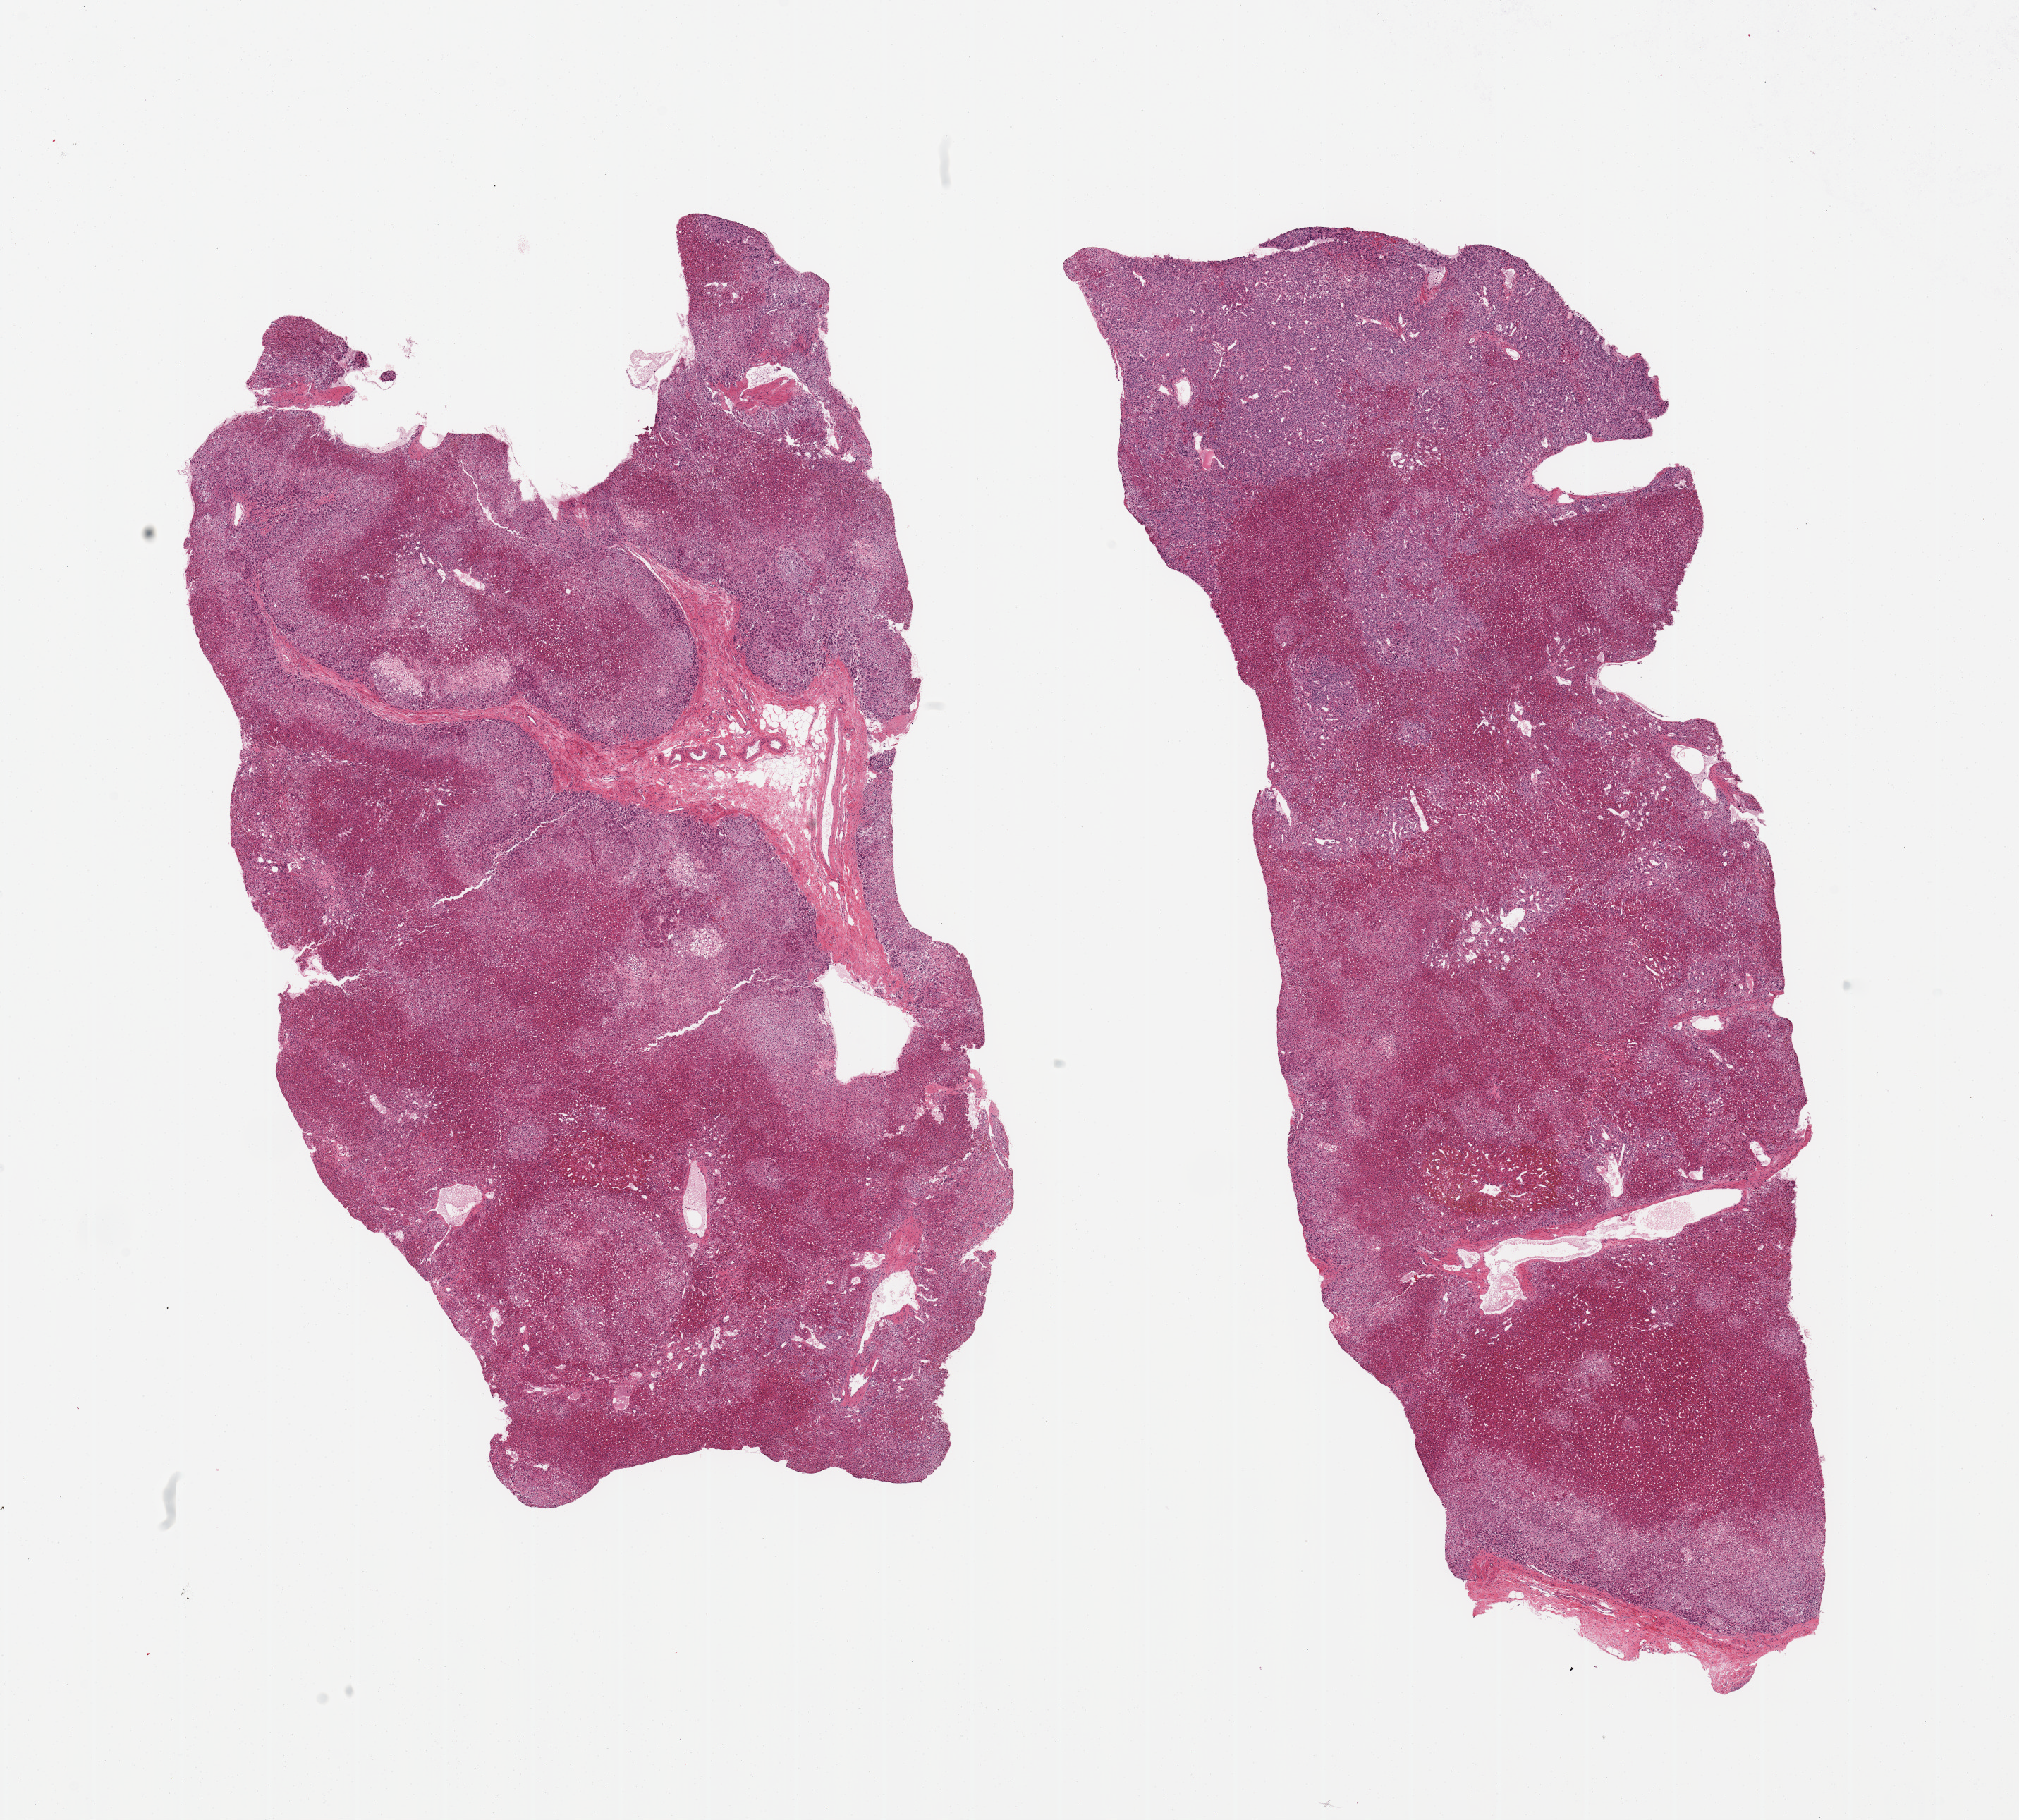
Digitized haematoxylin and eosin-stained section — a low-resolution overview of the entire scanned area, about 22.6 x 20.4 mm (acquisition: 20x scan). PAXgene-fixed, paraffin-embedded tissue. Sampled site (target tissue): adrenal gland. Donor tissue sample. Donor: female.
- reviewer comment on this tissue sample: 2 pieces, all cortex, minimal fat, well preserved